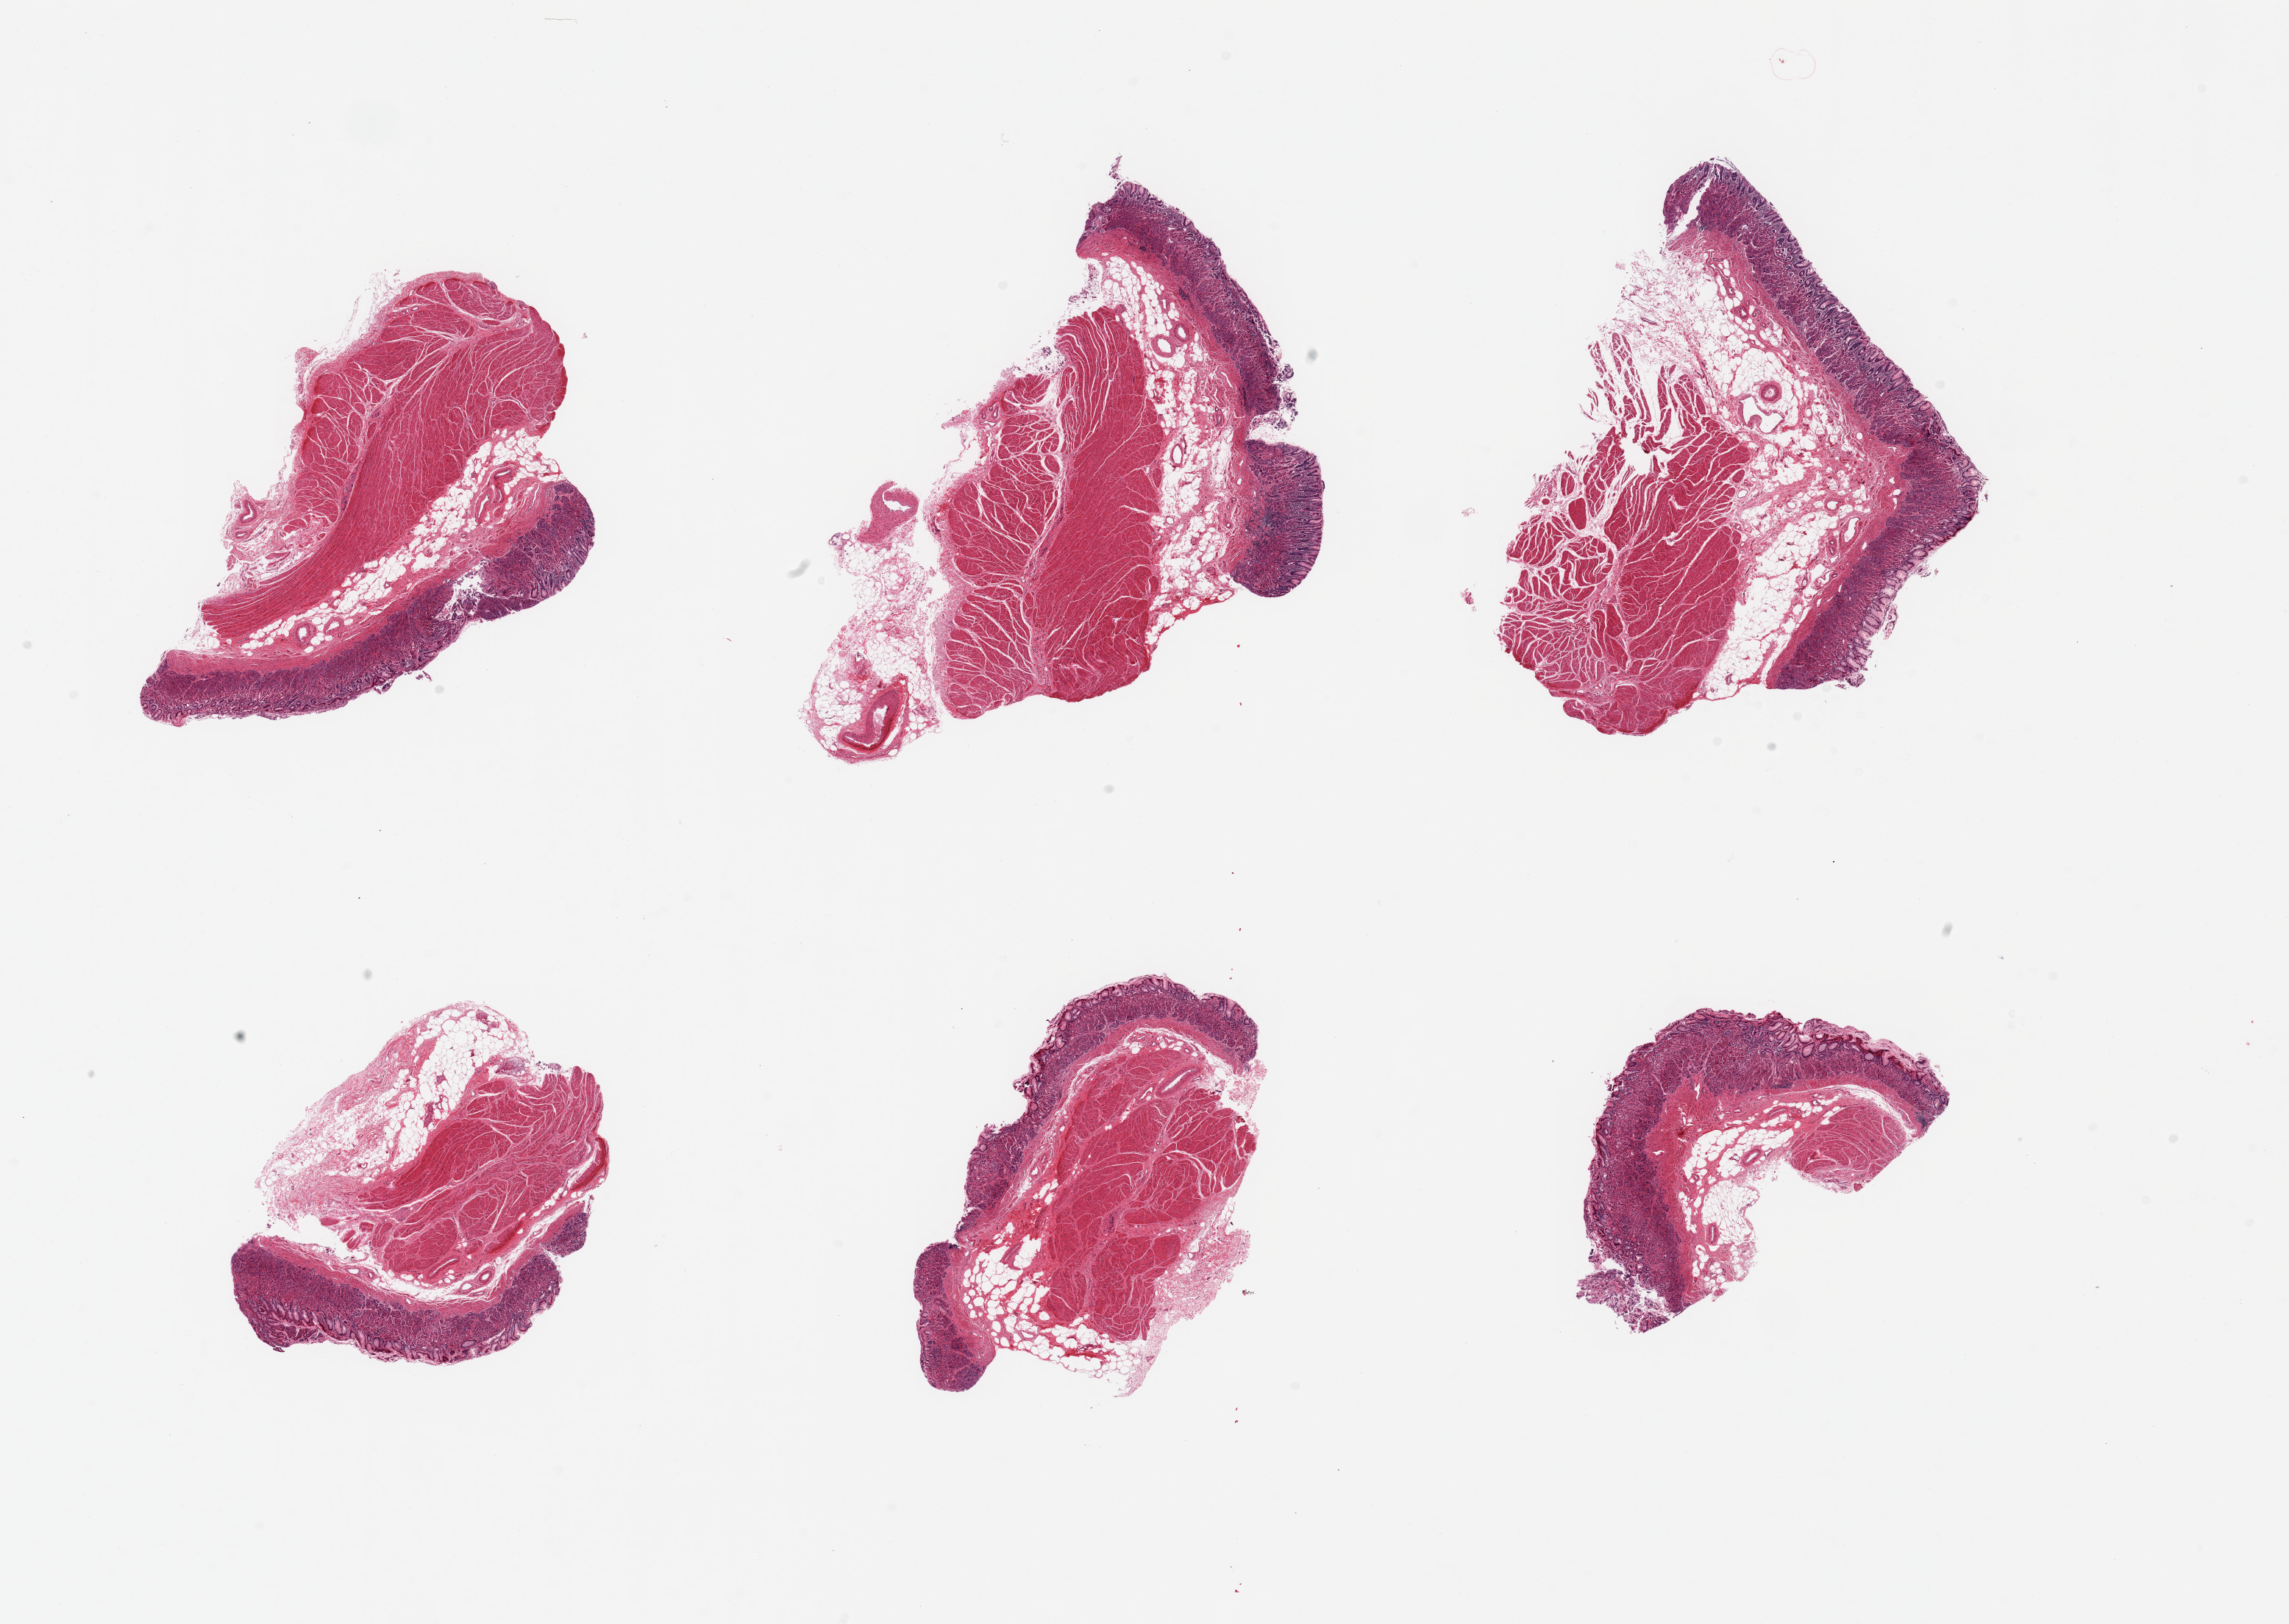
Haematoxylin and eosin whole-slide image, low-resolution overview of the scanned area, about 24.6 x 17.5 mm (from a 20x scan); PAXgene-fixed paraffin-embedded (PFPE) section; target tissue: gastroesophageal junction; donor tissue sample. Female donor.
* review note (as recorded): 6 pieces; all contain gastric mucosa and muscle